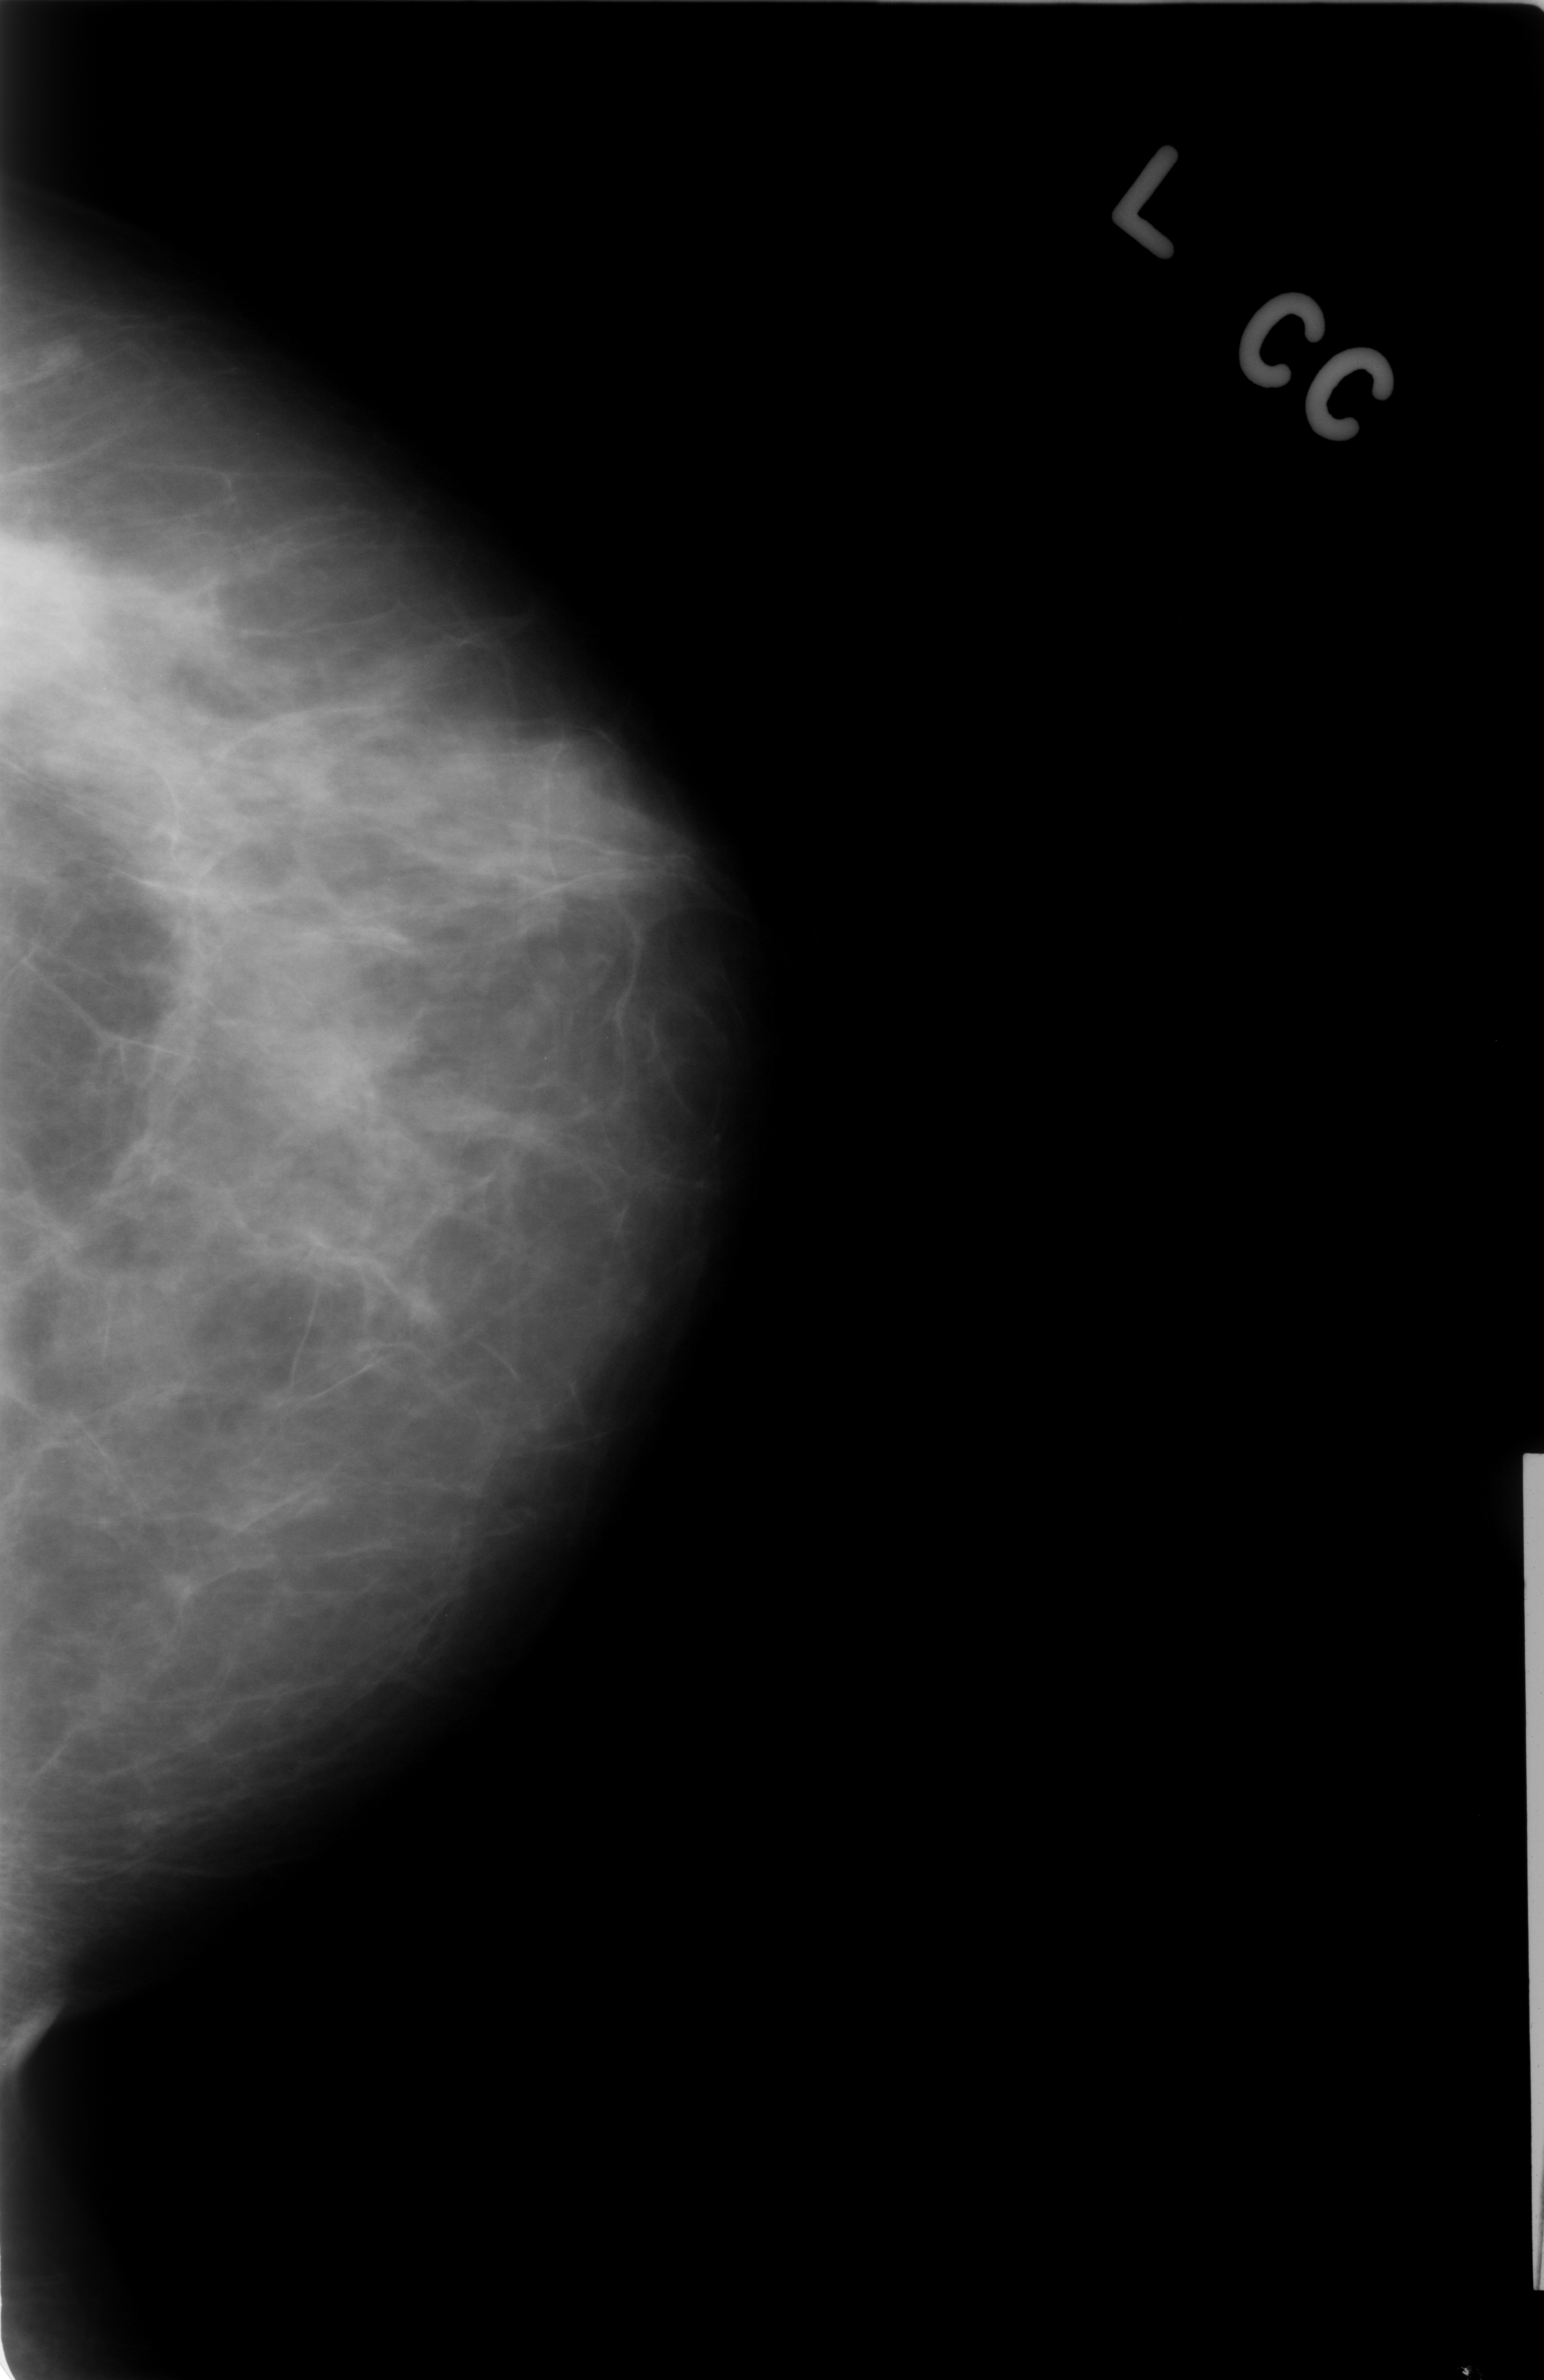
Mammogram (digitized film), left breast, CC view, BI-RADS breast density category 2 (scale 1–4).
Marked abnormality: mass, shape round, margins microlobulated; BI-RADS assessment category 3; benign; no additional work-up was recommended (benign without callback).